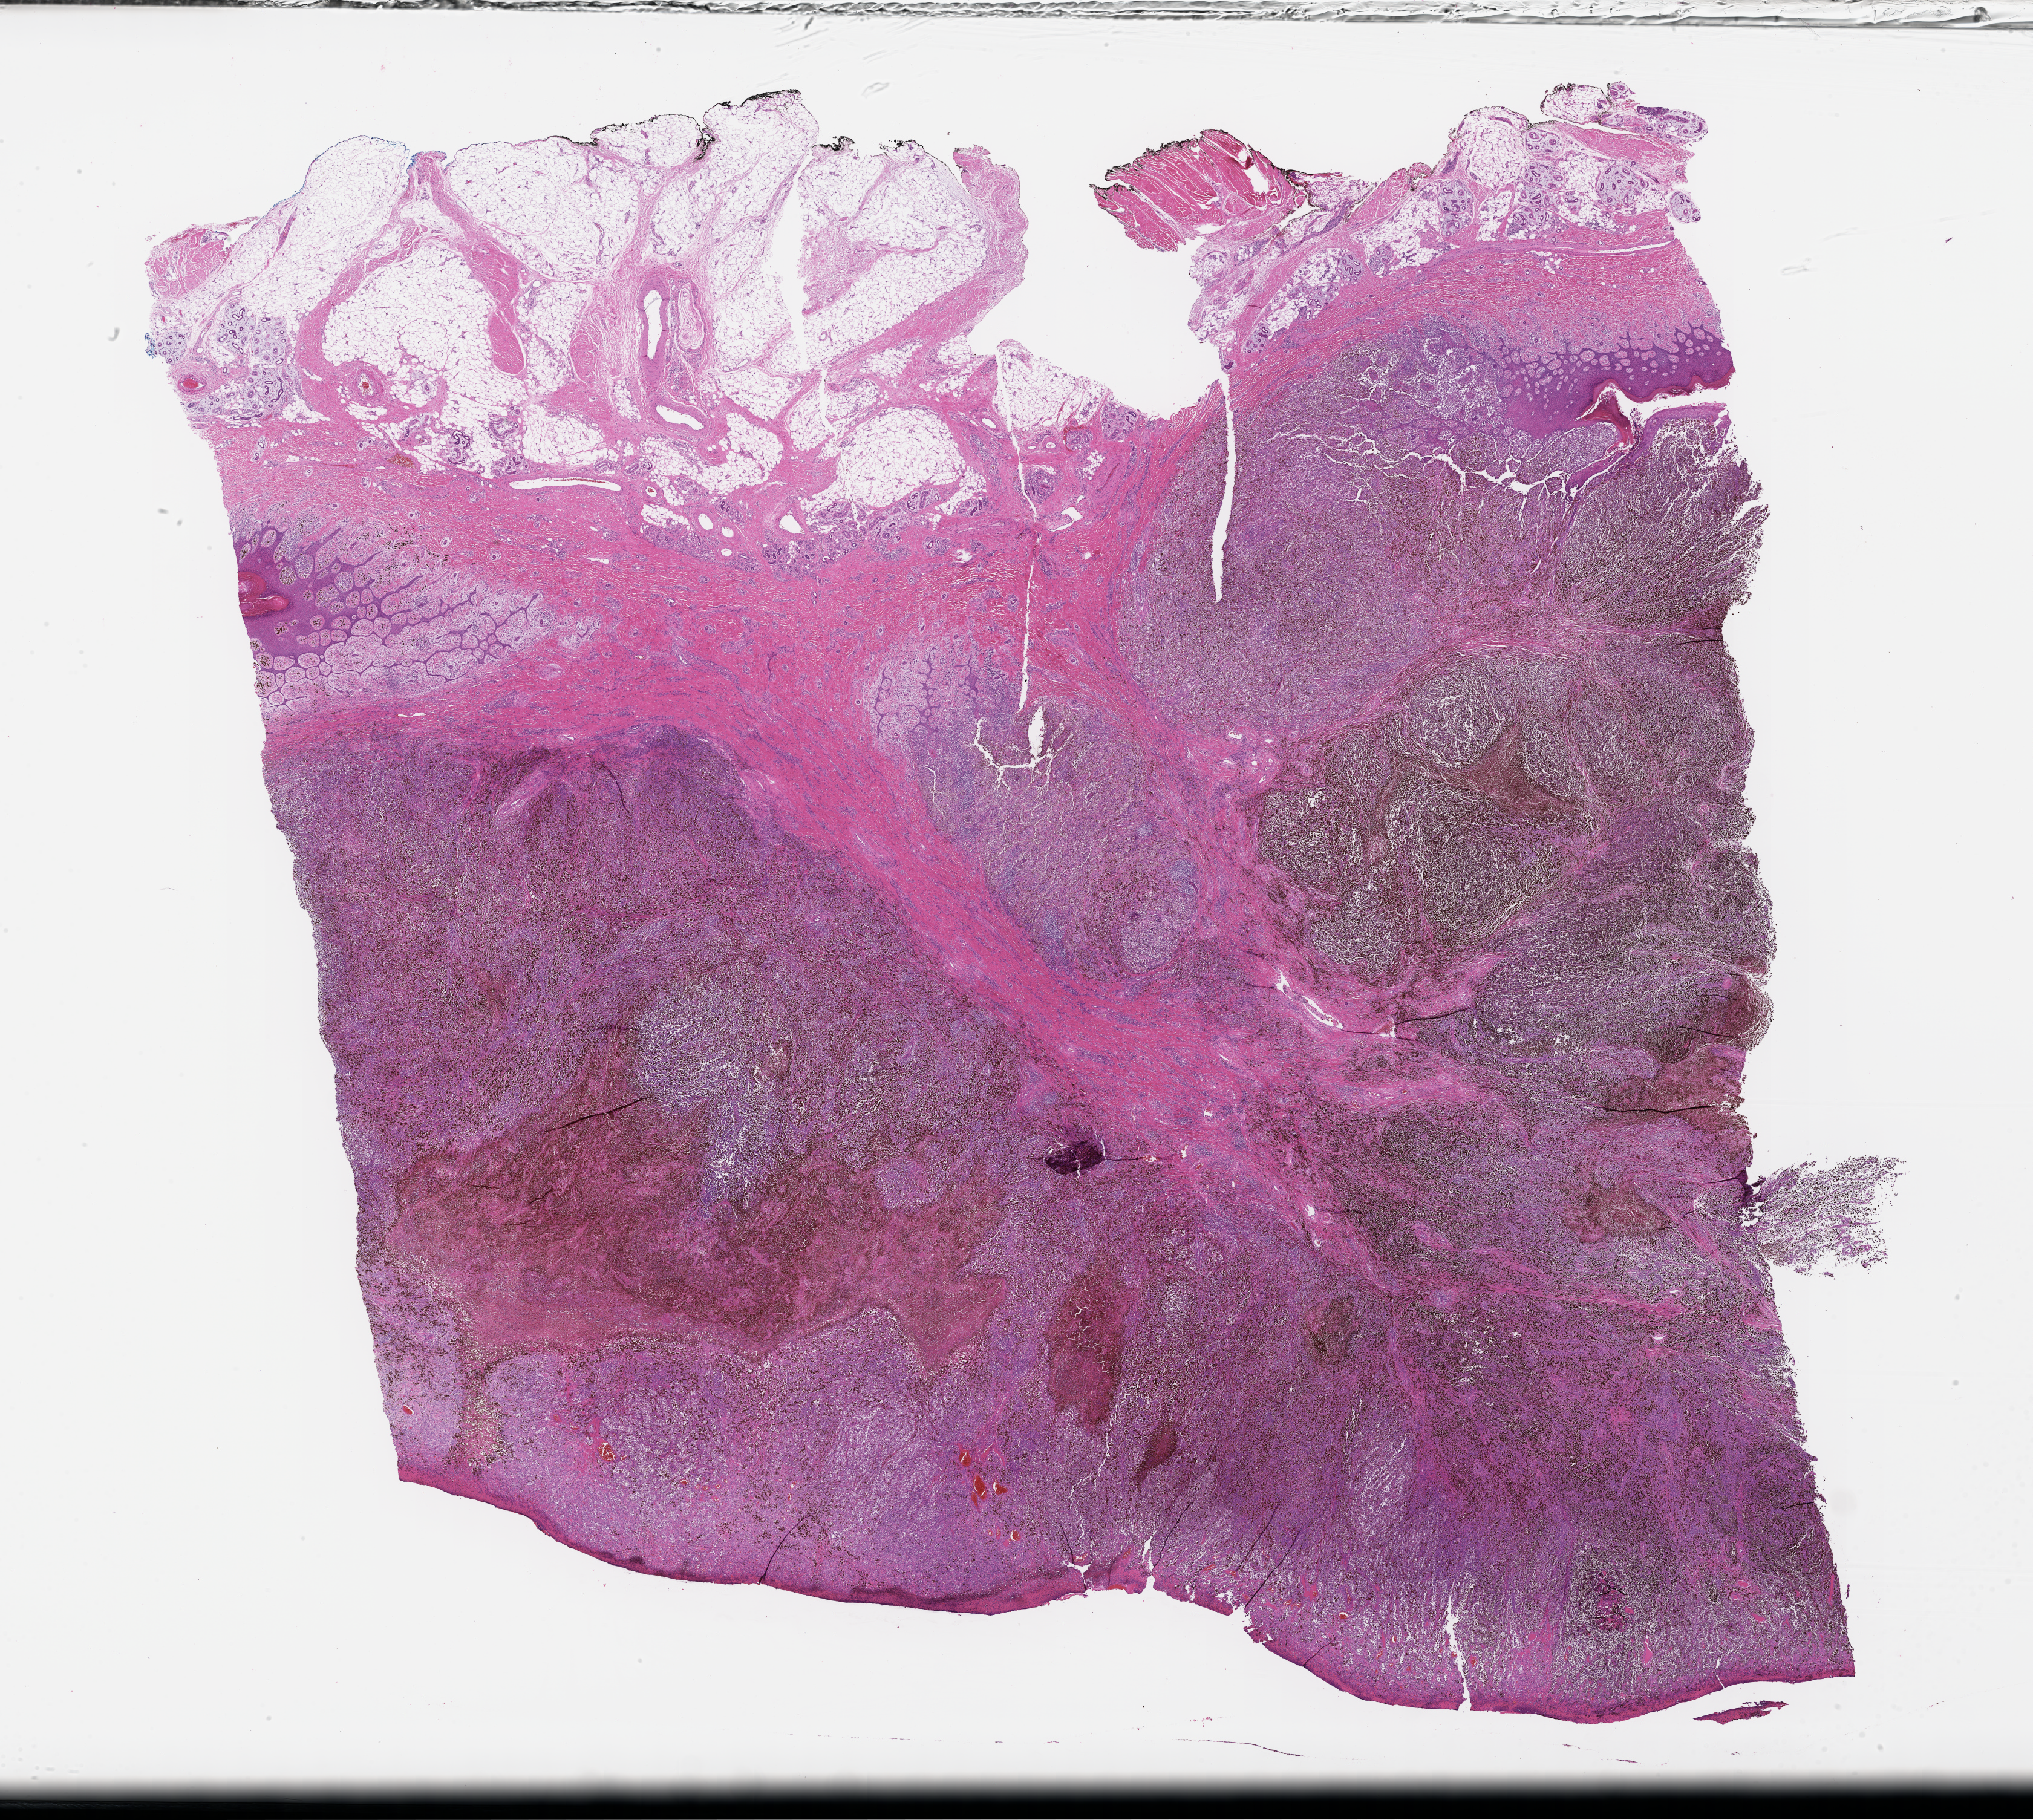
Whole-slide image, hematoxylin and eosin (H&E) stain, low-resolution overview of the scanned area, about 27.1 x 24.3 mm. Formalin-fixed, paraffin-embedded (FFPE) tissue. Site: skin. Patient sex: male.
This section: primary tumor. Diagnosis: Melanoma.